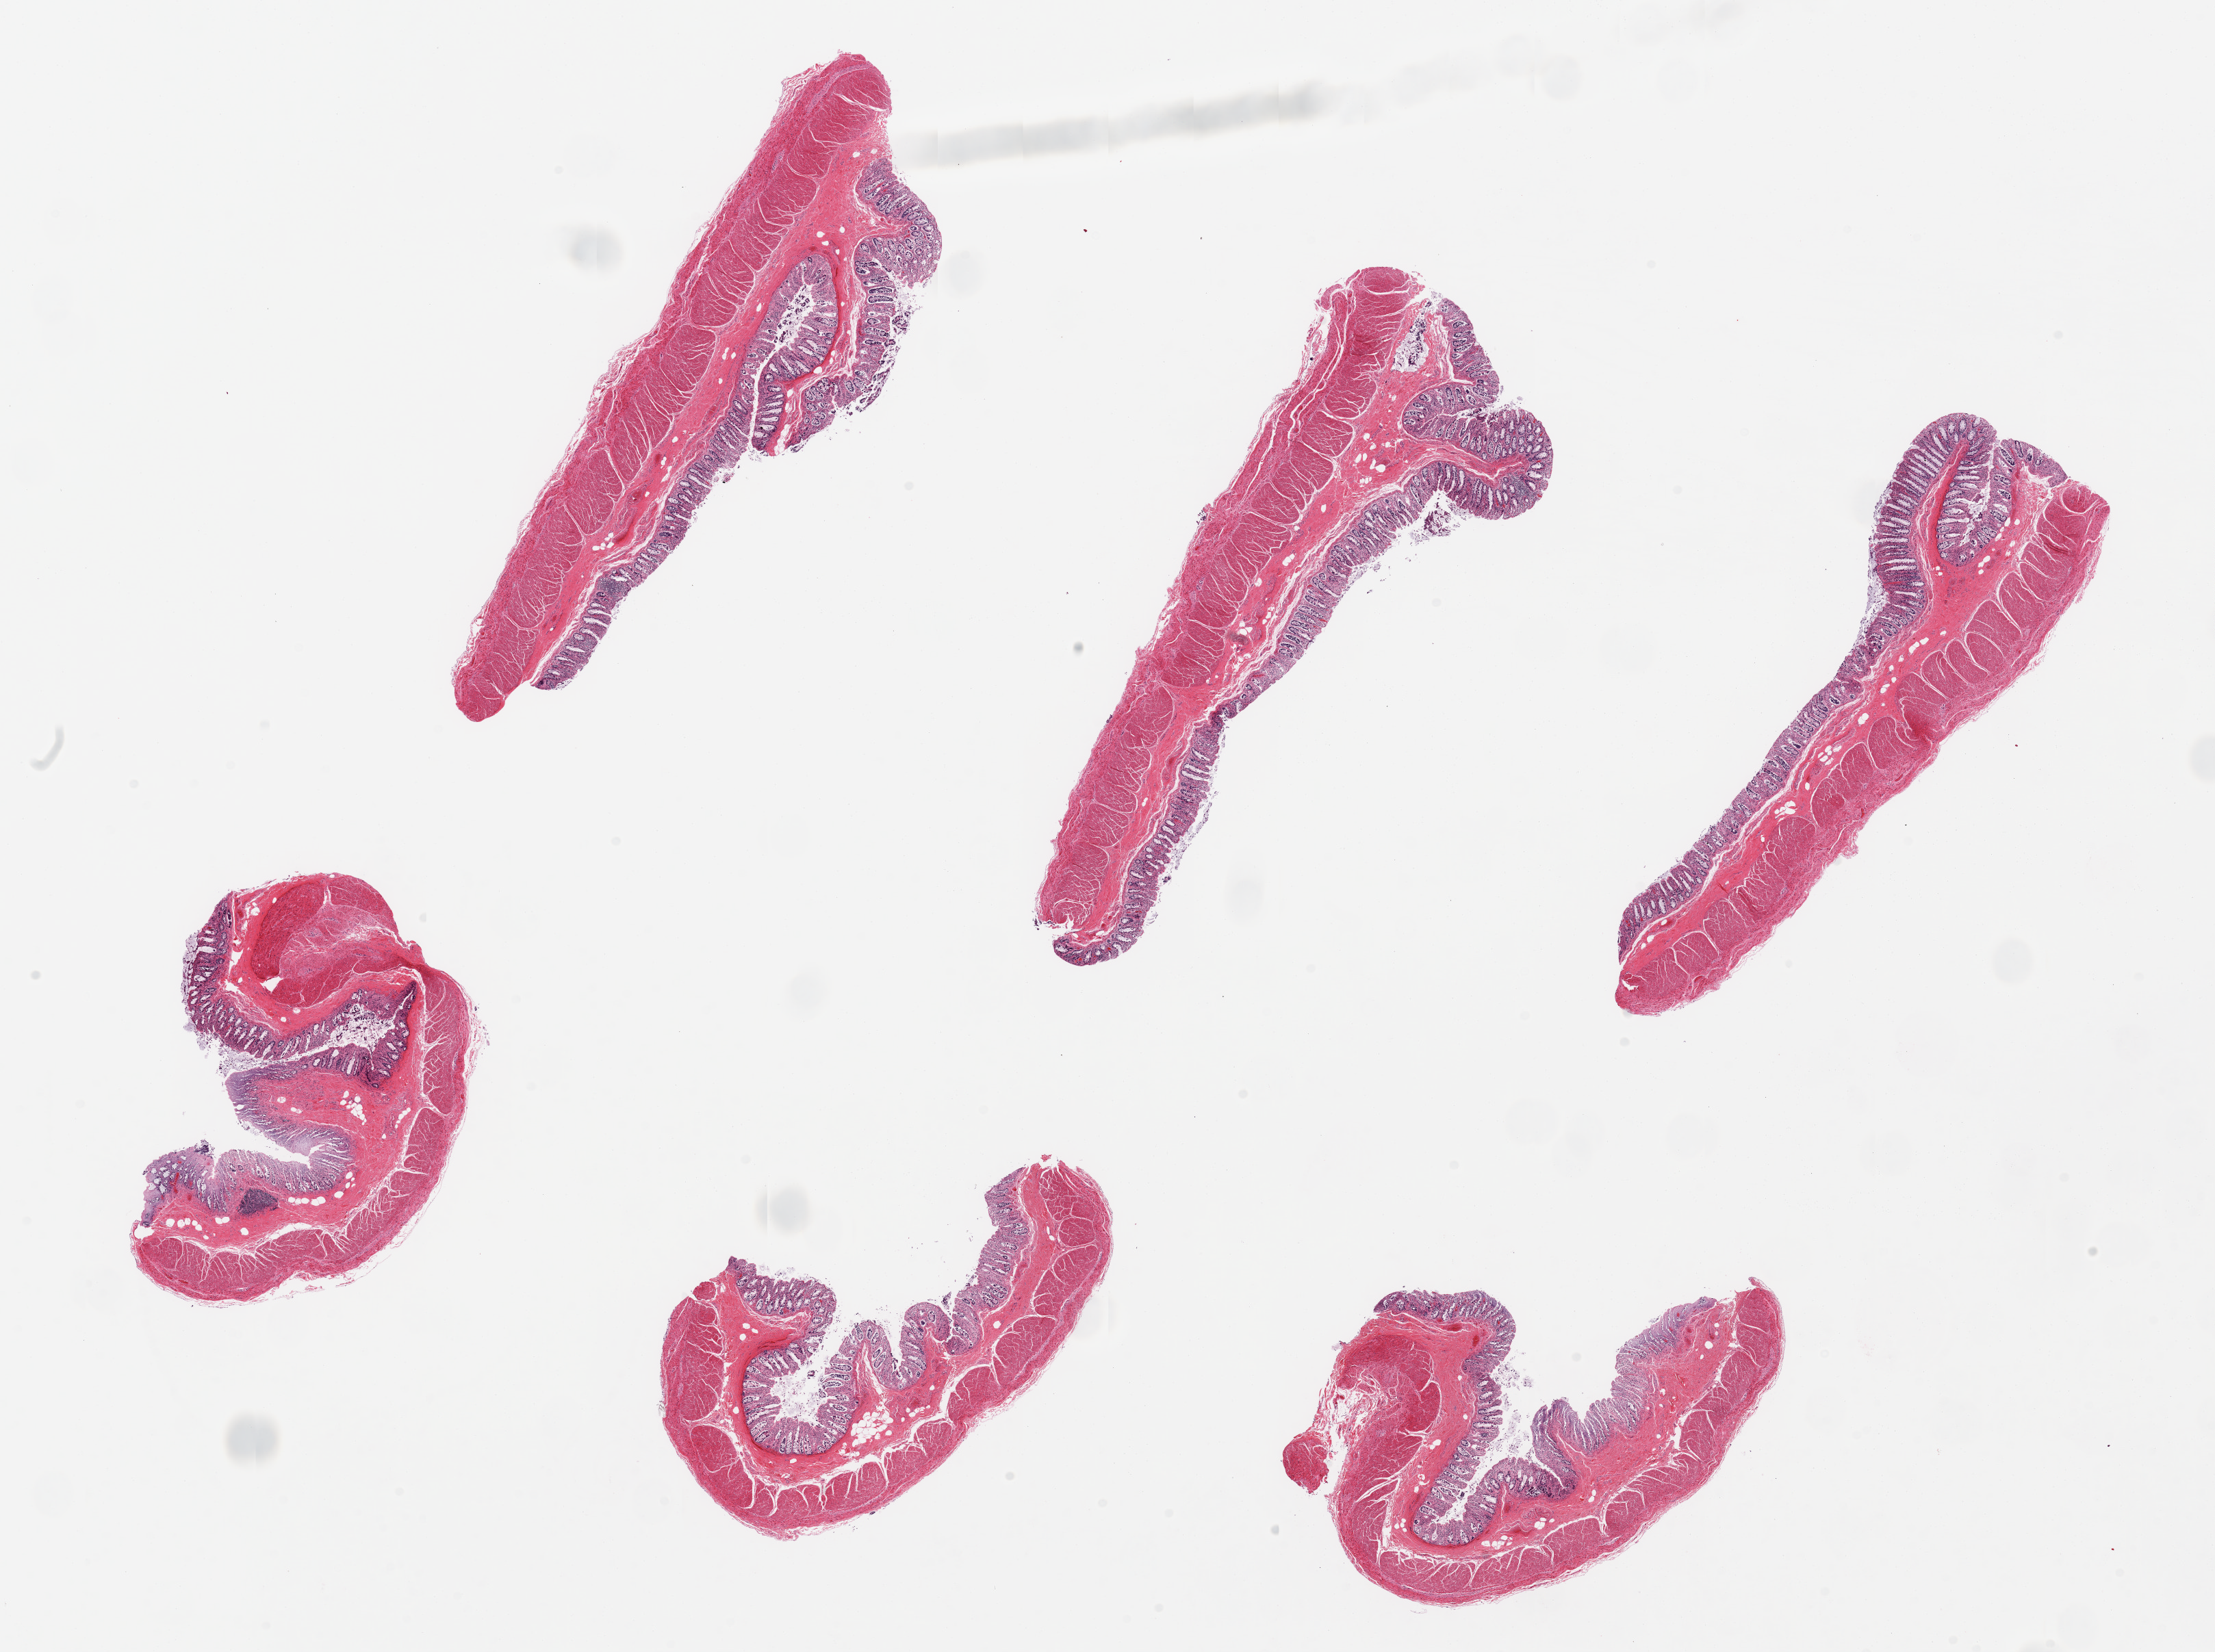
Whole-slide image, H&E stain — a low-resolution overview of the entire scanned area, about 25.6 x 19.1 mm (from a 20x scan); PAXgene-fixed, paraffin-embedded tissue; target tissue: transverse colon; tissue donor sample. Donor sex: male.
Pathologist's review note for this sample: 6 pieces, full thickness colon, moderately to severely autolyzed mucosa.